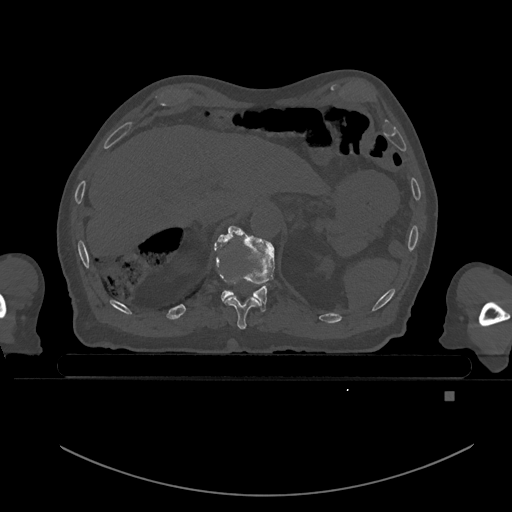
CT including the spine, one axial slice. Bone window (W 1800 / L 400 HU). 0.5 mm slice thickness. 512 × 512 image matrix. Patient: male, 82 years. Case-level facts recorded for this patient, not image findings: primary cancer: prostate; vertebrae with lytic lesions (as recorded): T11, T9, T8, T2.
Structures marked on this image (semi-automatically segmented with operator editing):
- T10 vertebra: bounding box (x1, y1, x2, y2) in pixels: (215, 241, 260, 330)
- T11 vertebra: (218, 225, 275, 312)